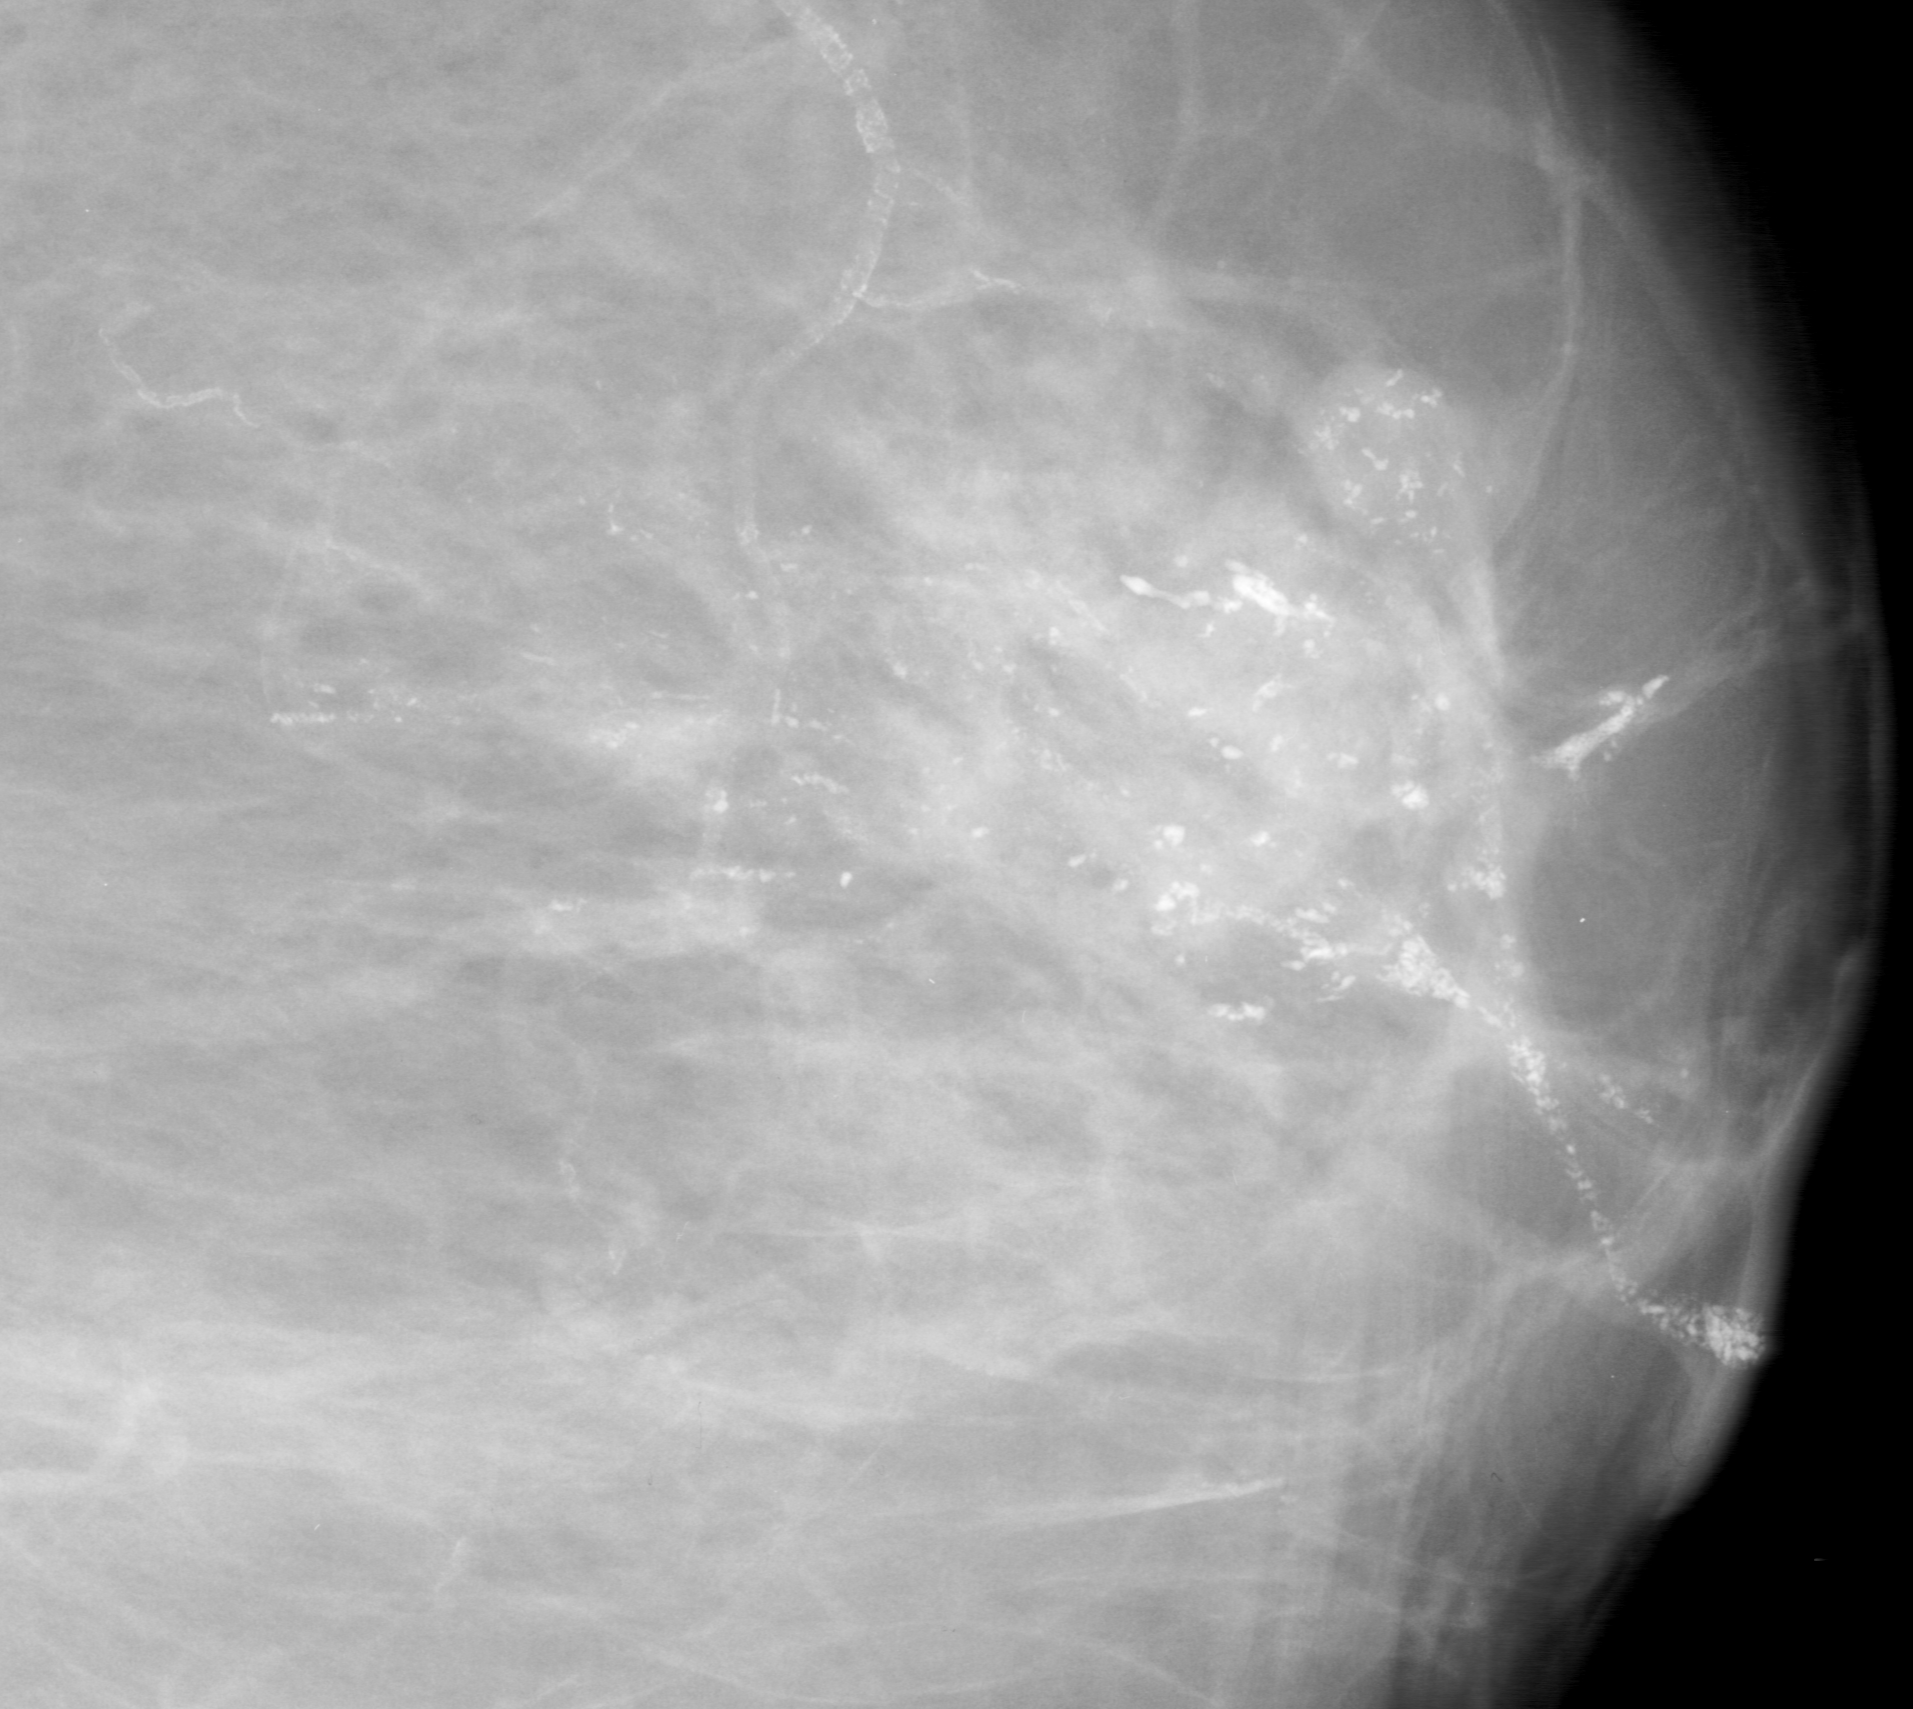
Region of interest cut from a scanned film mammogram (one marked finding), left breast, MLO view.
- Calcifications, morphology pleomorphic, distribution linear; BI-RADS assessment category 5; pathology (as recorded): malignant.